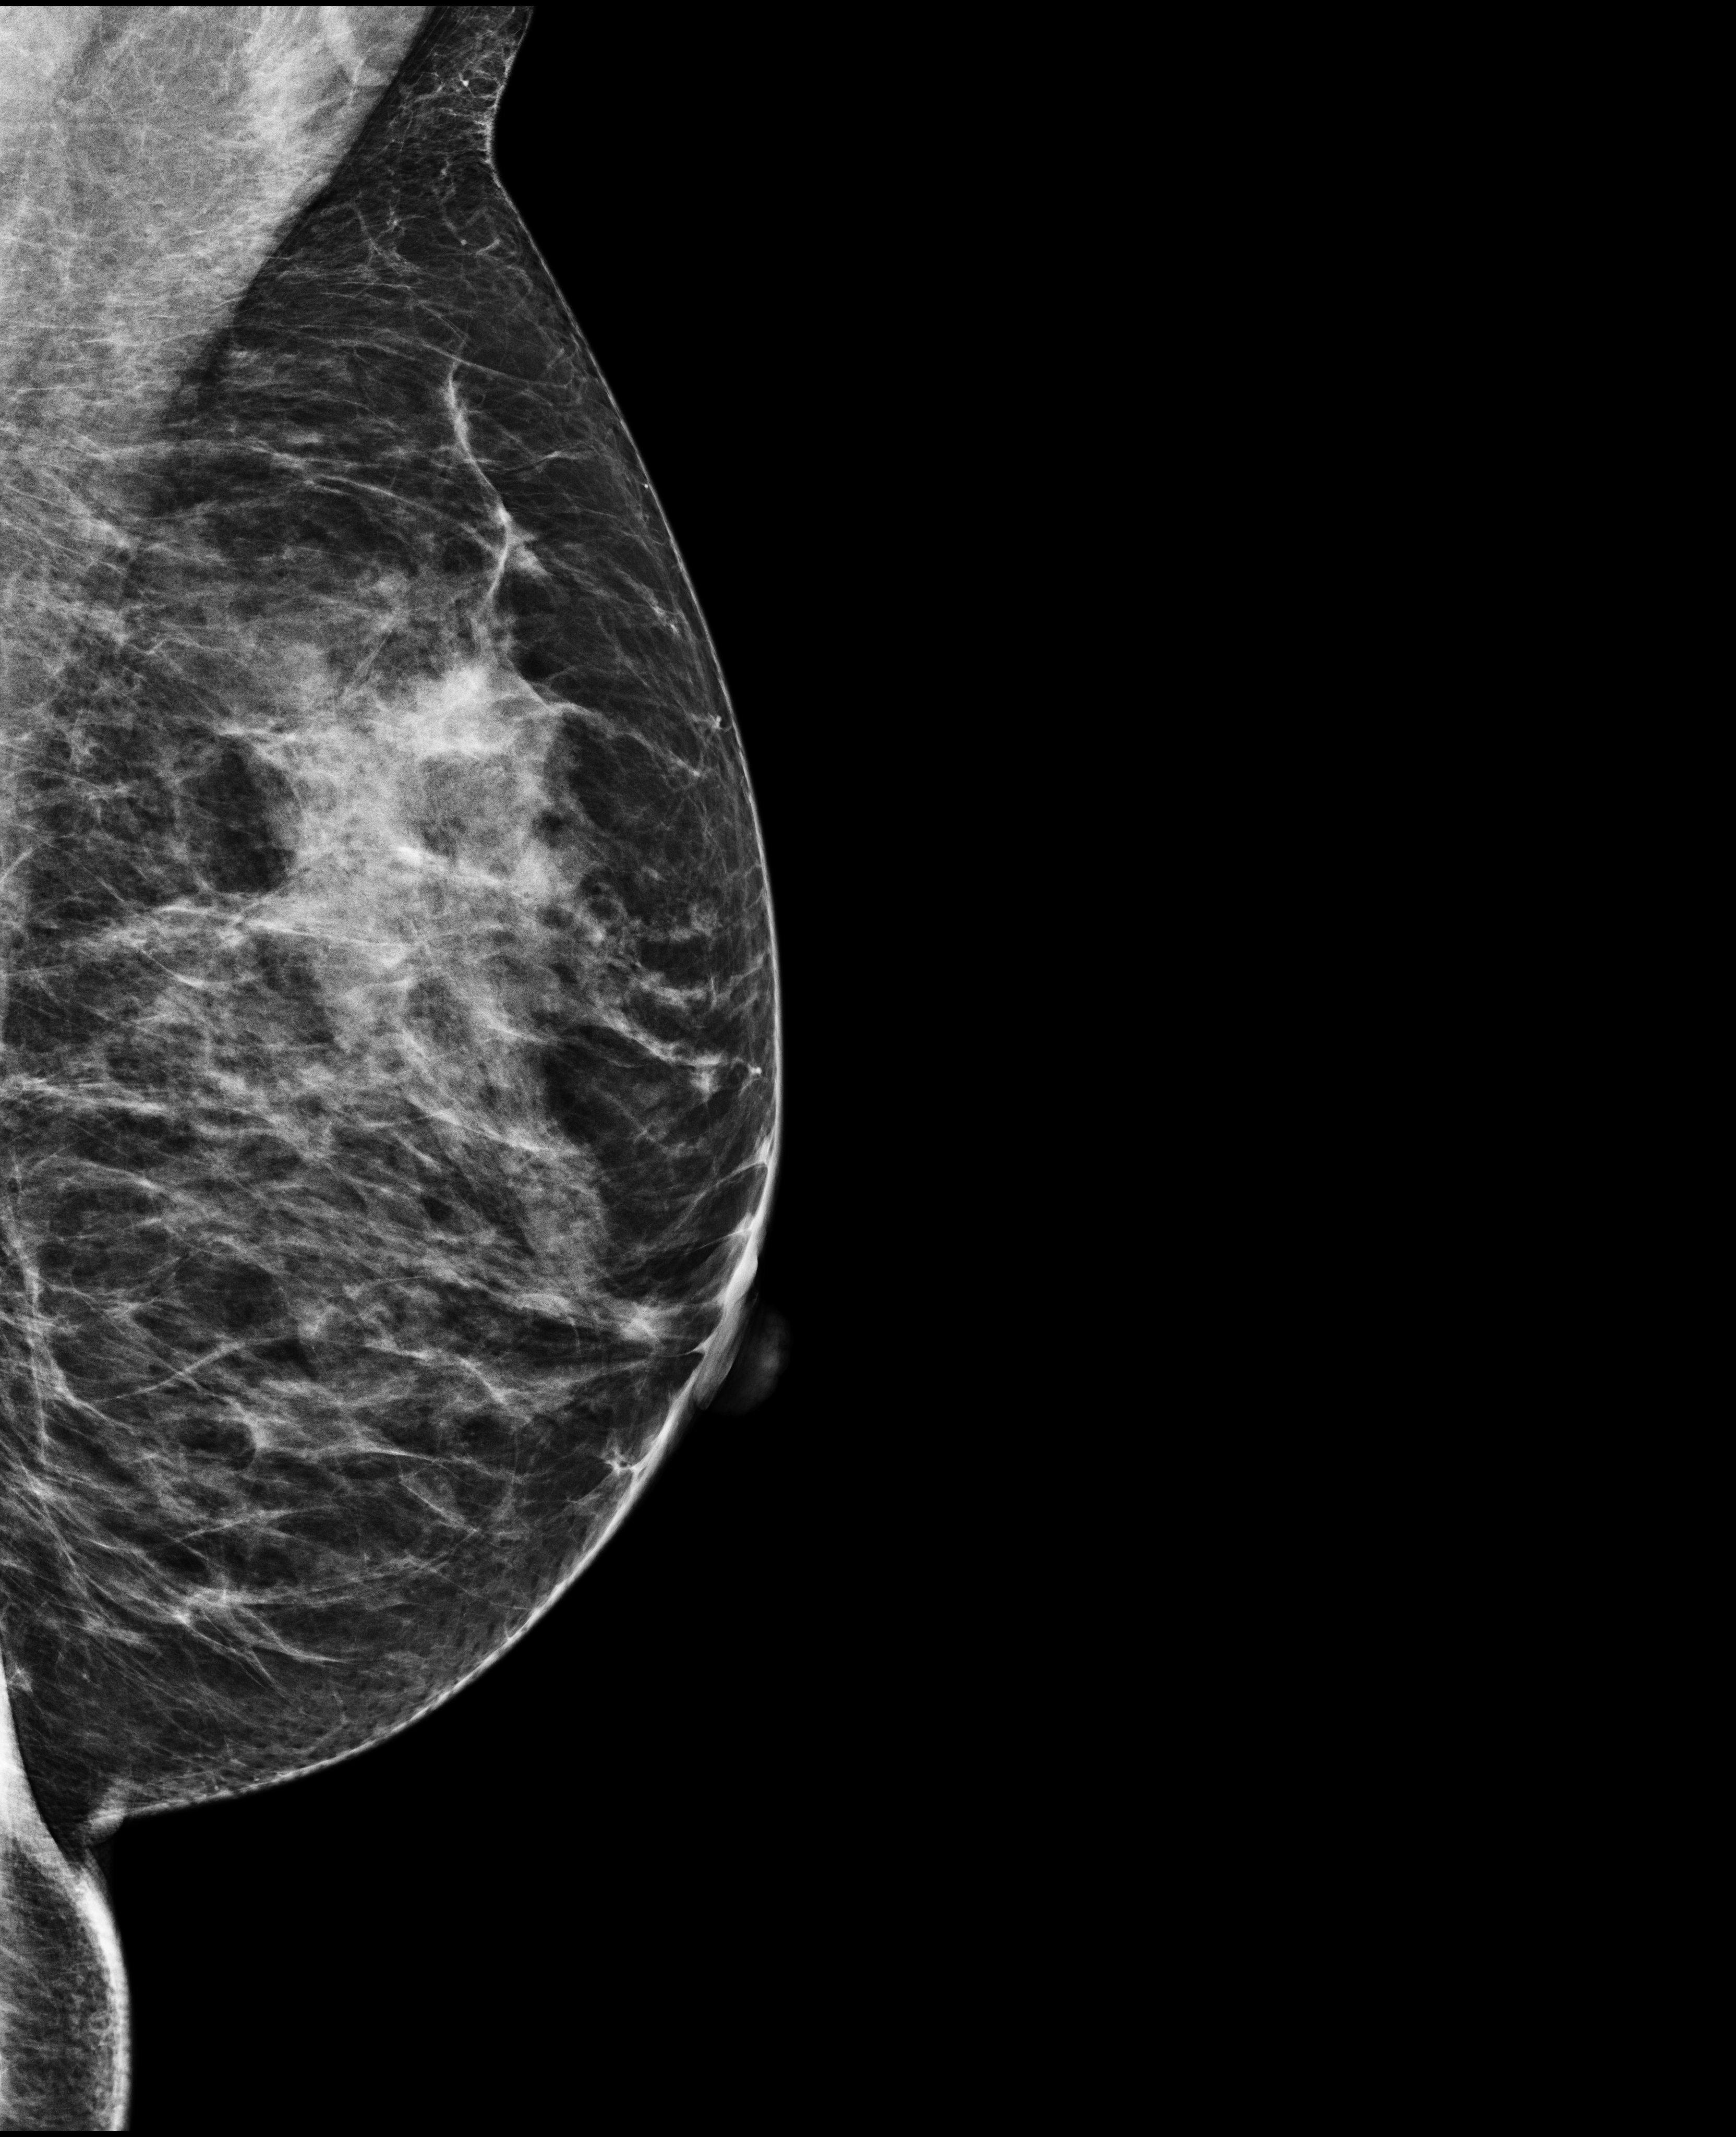
Full-field digital mammogram (FFDM); left breast; mediolateral oblique (MLO) view; annual screening mammography examination. Female patient, age 45 years.
- BI-RADS breast density category at the screening exam (both breasts, scale 1–4): 3
- final BI-RADS category for the screening round (tomosynthesis exam, both breasts): category 1
- recall: no recall after this screen